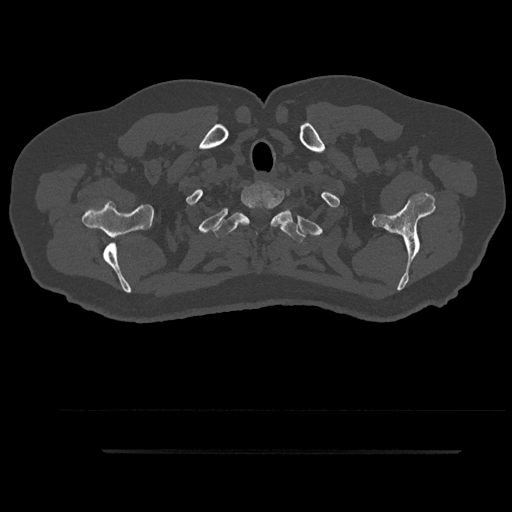
CT including the spine, one axial slice; position 779 of 797 along the scan axis; 120 kVp; bone window (W 1800 / L 400 HU); 0.5 mm slice thickness; 512 × 512 image matrix, field of view 432 × 432 mm. Male patient, age 63 years. From the clinical record (not read from this slice): primary cancer: renal; vertebrae with lytic lesions (as recorded): T8.
Annotated regions visible in this slice (semi-automatically segmented with operator editing):
- T1 vertebra: box from (x=232, y=185) to (x=284, y=226) px
- T2 vertebra: (x=213, y=206)–(x=306, y=241)